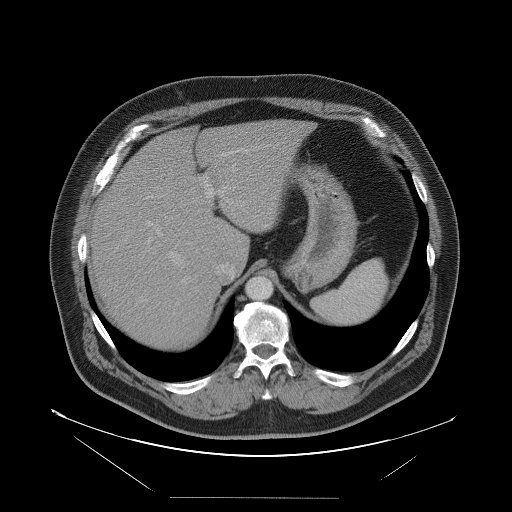
Contrast-enhanced abdominal CT, one axial slice. Position 74 of 114 along the scan axis. Intravenous contrast given. Soft-tissue window (W 400 / L 40 HU). 5 mm slice thickness. 512 × 512 image matrix, field of view 500 × 500 mm. Male patient, age 61 years. Case-level facts recorded for this patient, not image findings: diagnosis: colorectal cancer liver metastases, imaged before liver resection; multiple liver metastases: no; largest metastasis: 6.5 cm; disease in both lobes: yes.
Structures marked on this image (expert manual segmentation):
- hepatic veins: bounding box [x1, y1, x2, y2] px = [158, 164, 250, 284]
- liver: [89, 121, 311, 350]
- planned liver remnant (the part of the liver to remain after resection): [146, 121, 311, 265]
- portal vein (with intrahepatic branches): [141, 148, 249, 302]